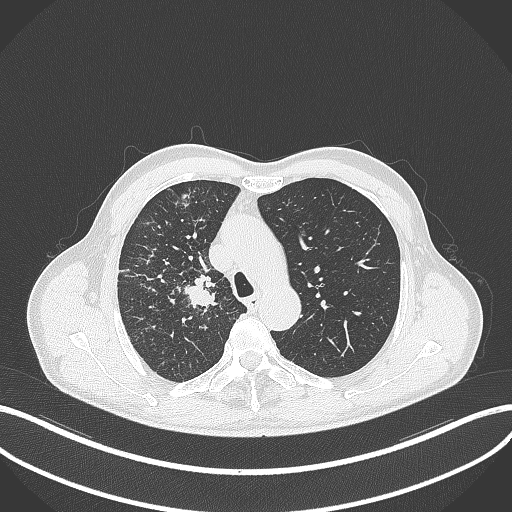
Chest CT, one axial slice; slice 354 of 490 in the series (ordered by position); reconstruction kernel B70f; 120 kVp; lung window (W 1500 / L -600 HU); 1 mm slice thickness; 512 × 512 image matrix. Male patient, age 69 years. From the clinical record (not read from this slice): clinical TNM (as recorded): T2a N0 M0.
Structures marked on this image (rectangle marked by the reading radiologist):
- lung tumour (recorded histology: adenocarcinoma): bounding box (x1, y1, x2, y2) in pixels: (180, 265, 222, 311)